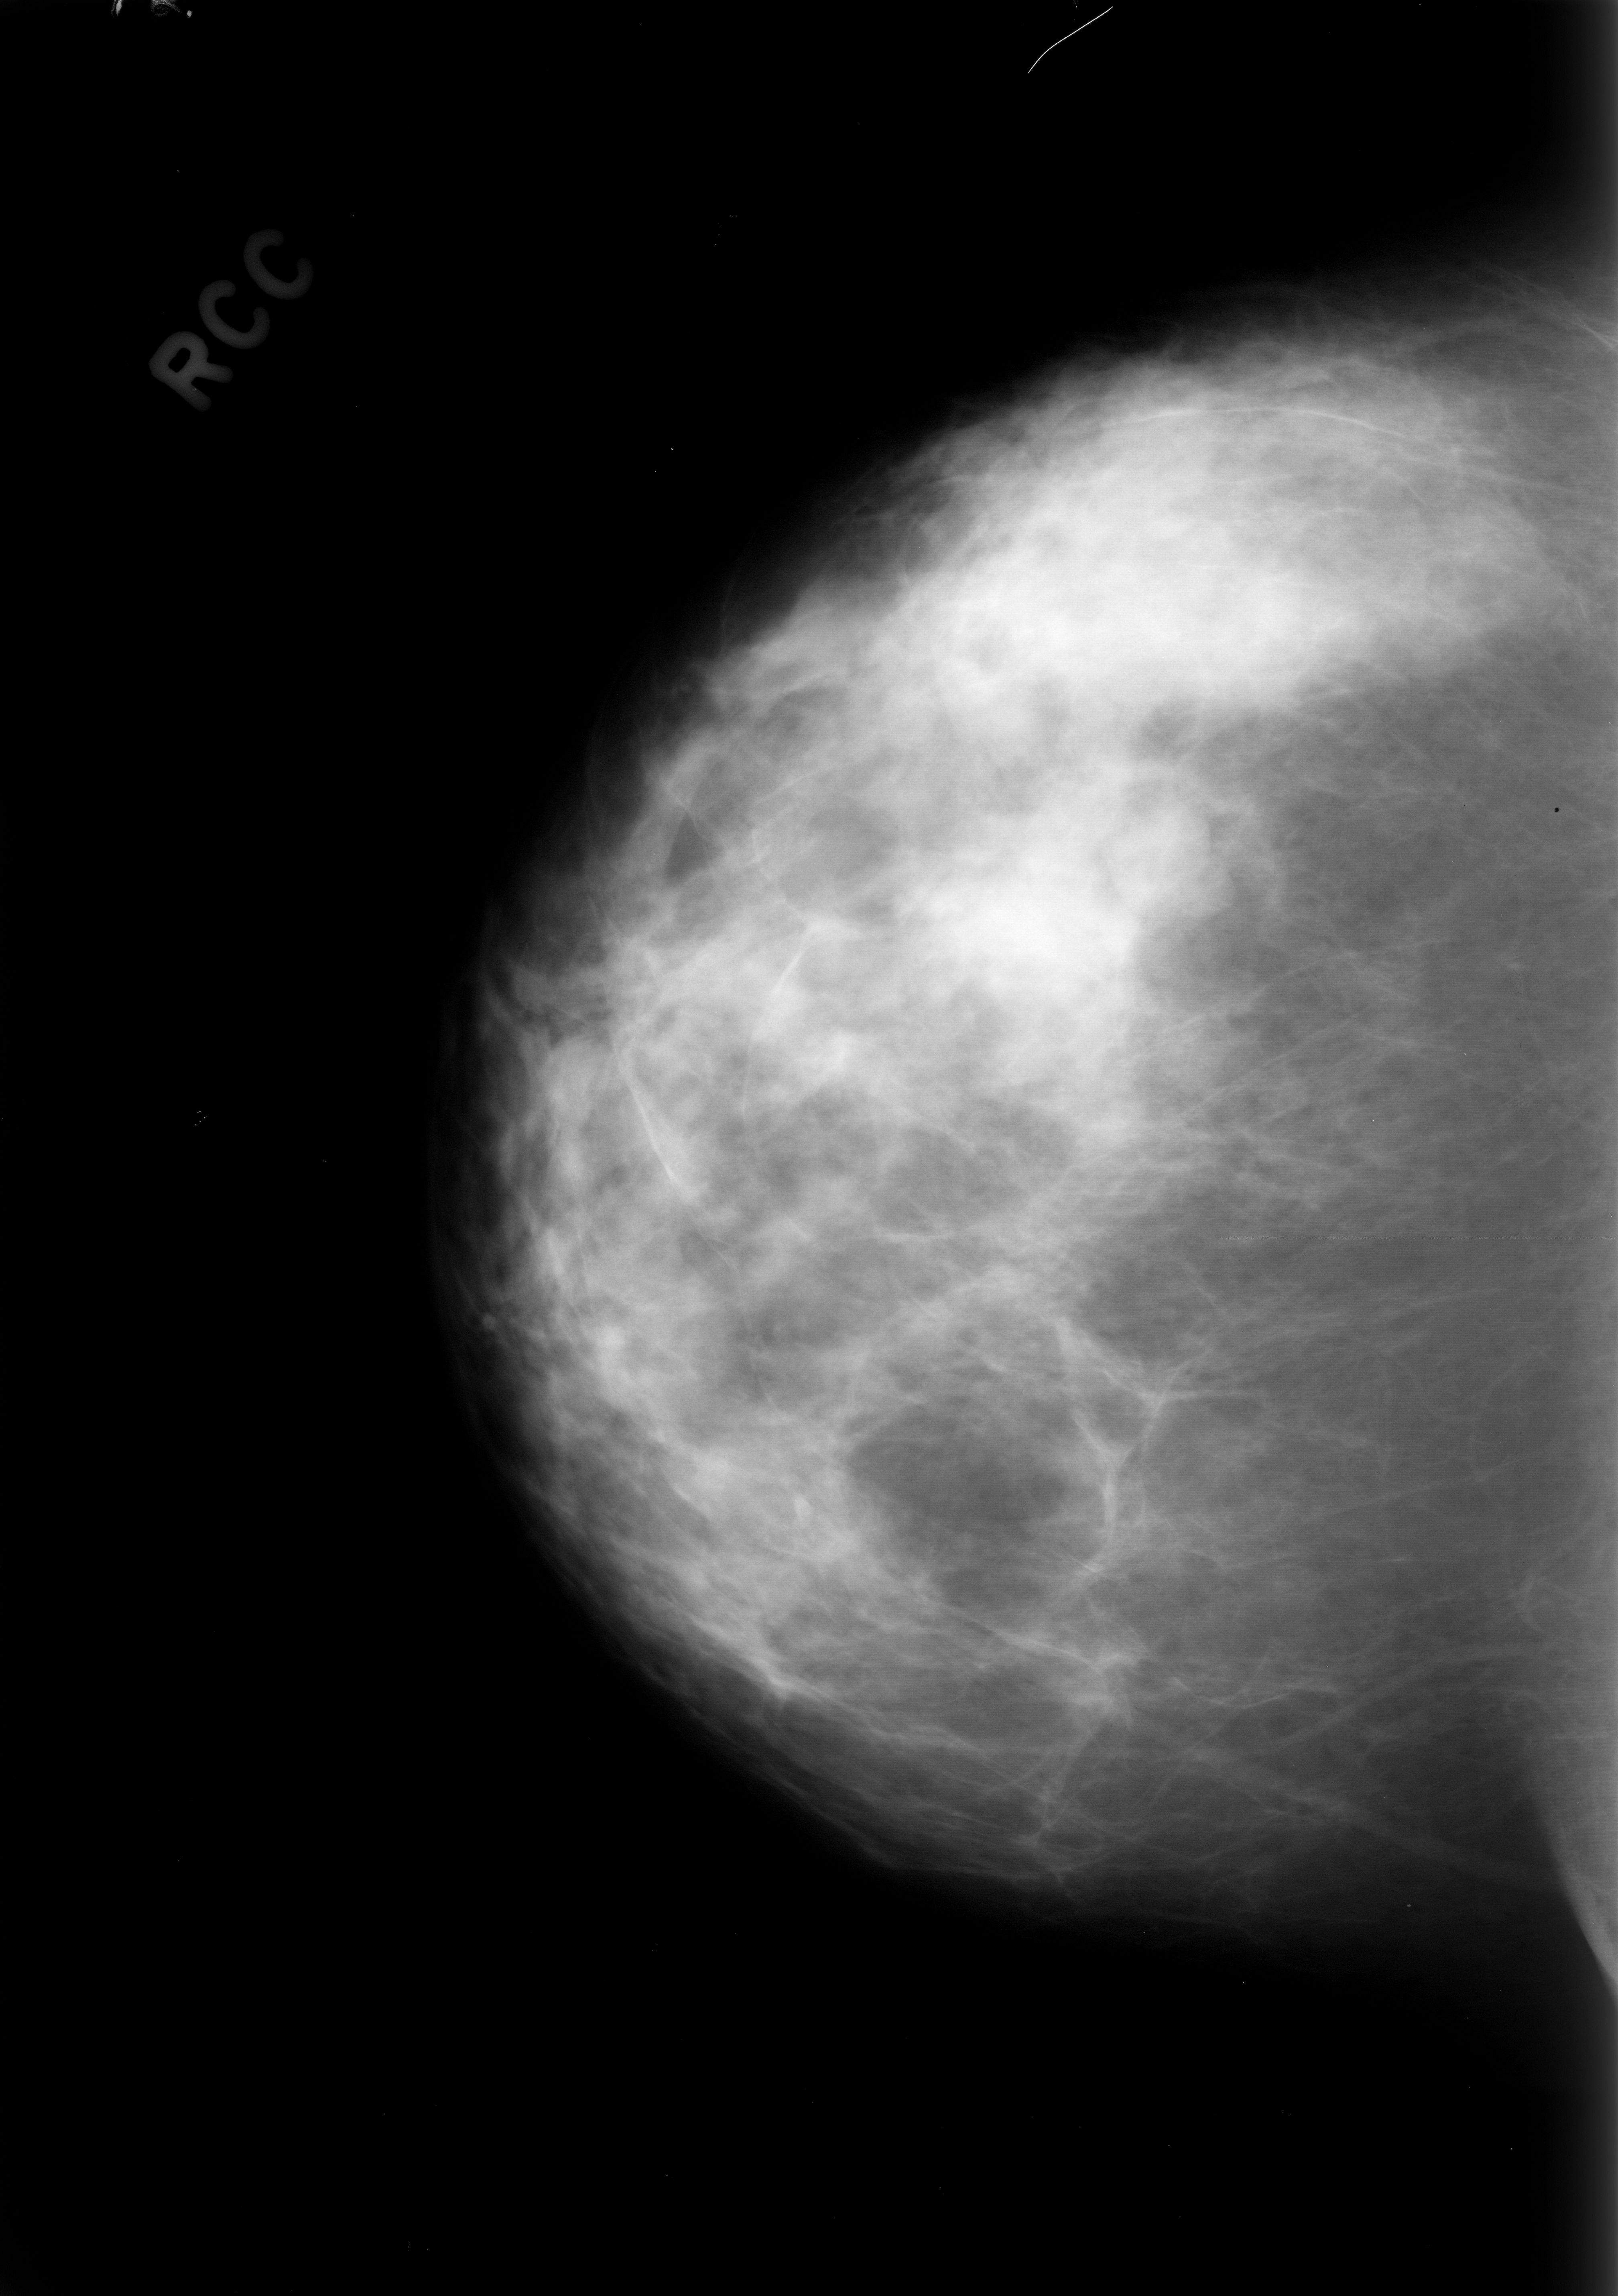
Digitized screen-film mammogram; right breast; CC view; 1618 × 2296 image matrix.
Expert-marked regions of interest on this film, with their recorded descriptors:
- mass, shape lobulated, margins circumscribed; BI-RADS assessment category 3; pathology (as recorded): benign: bounding box (x1, y1, x2, y2) in pixels: (1111, 791, 1244, 933)